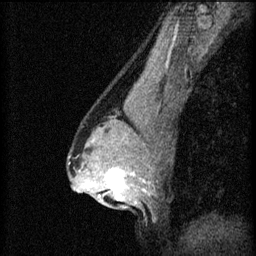
Breast MRI (dynamic contrast-enhanced), one sagittal slice; slice 39 of 60 in the series (ordered by position); 3 images stored at this slice position (order not interpretable as contrast timing); 1.5 T; TE 4.2 ms, TR 8.2 ms; 2 mm slice thickness; 256 × 256 image matrix, field of view 180 × 180 mm. Patient: female, 44 years.
Outlined on this slice (semi-automatically segmented with operator editing):
- analysis volume of interest (the breast-tissue region the enhancement analysis was run in; not a lesion): bounding box [x1, y1, x2, y2] px = [94, 162, 143, 205]
- tumour enhancement mask (voxels above the 70 % enhancement threshold inside the analysis volume of interest): [98, 168, 135, 201]